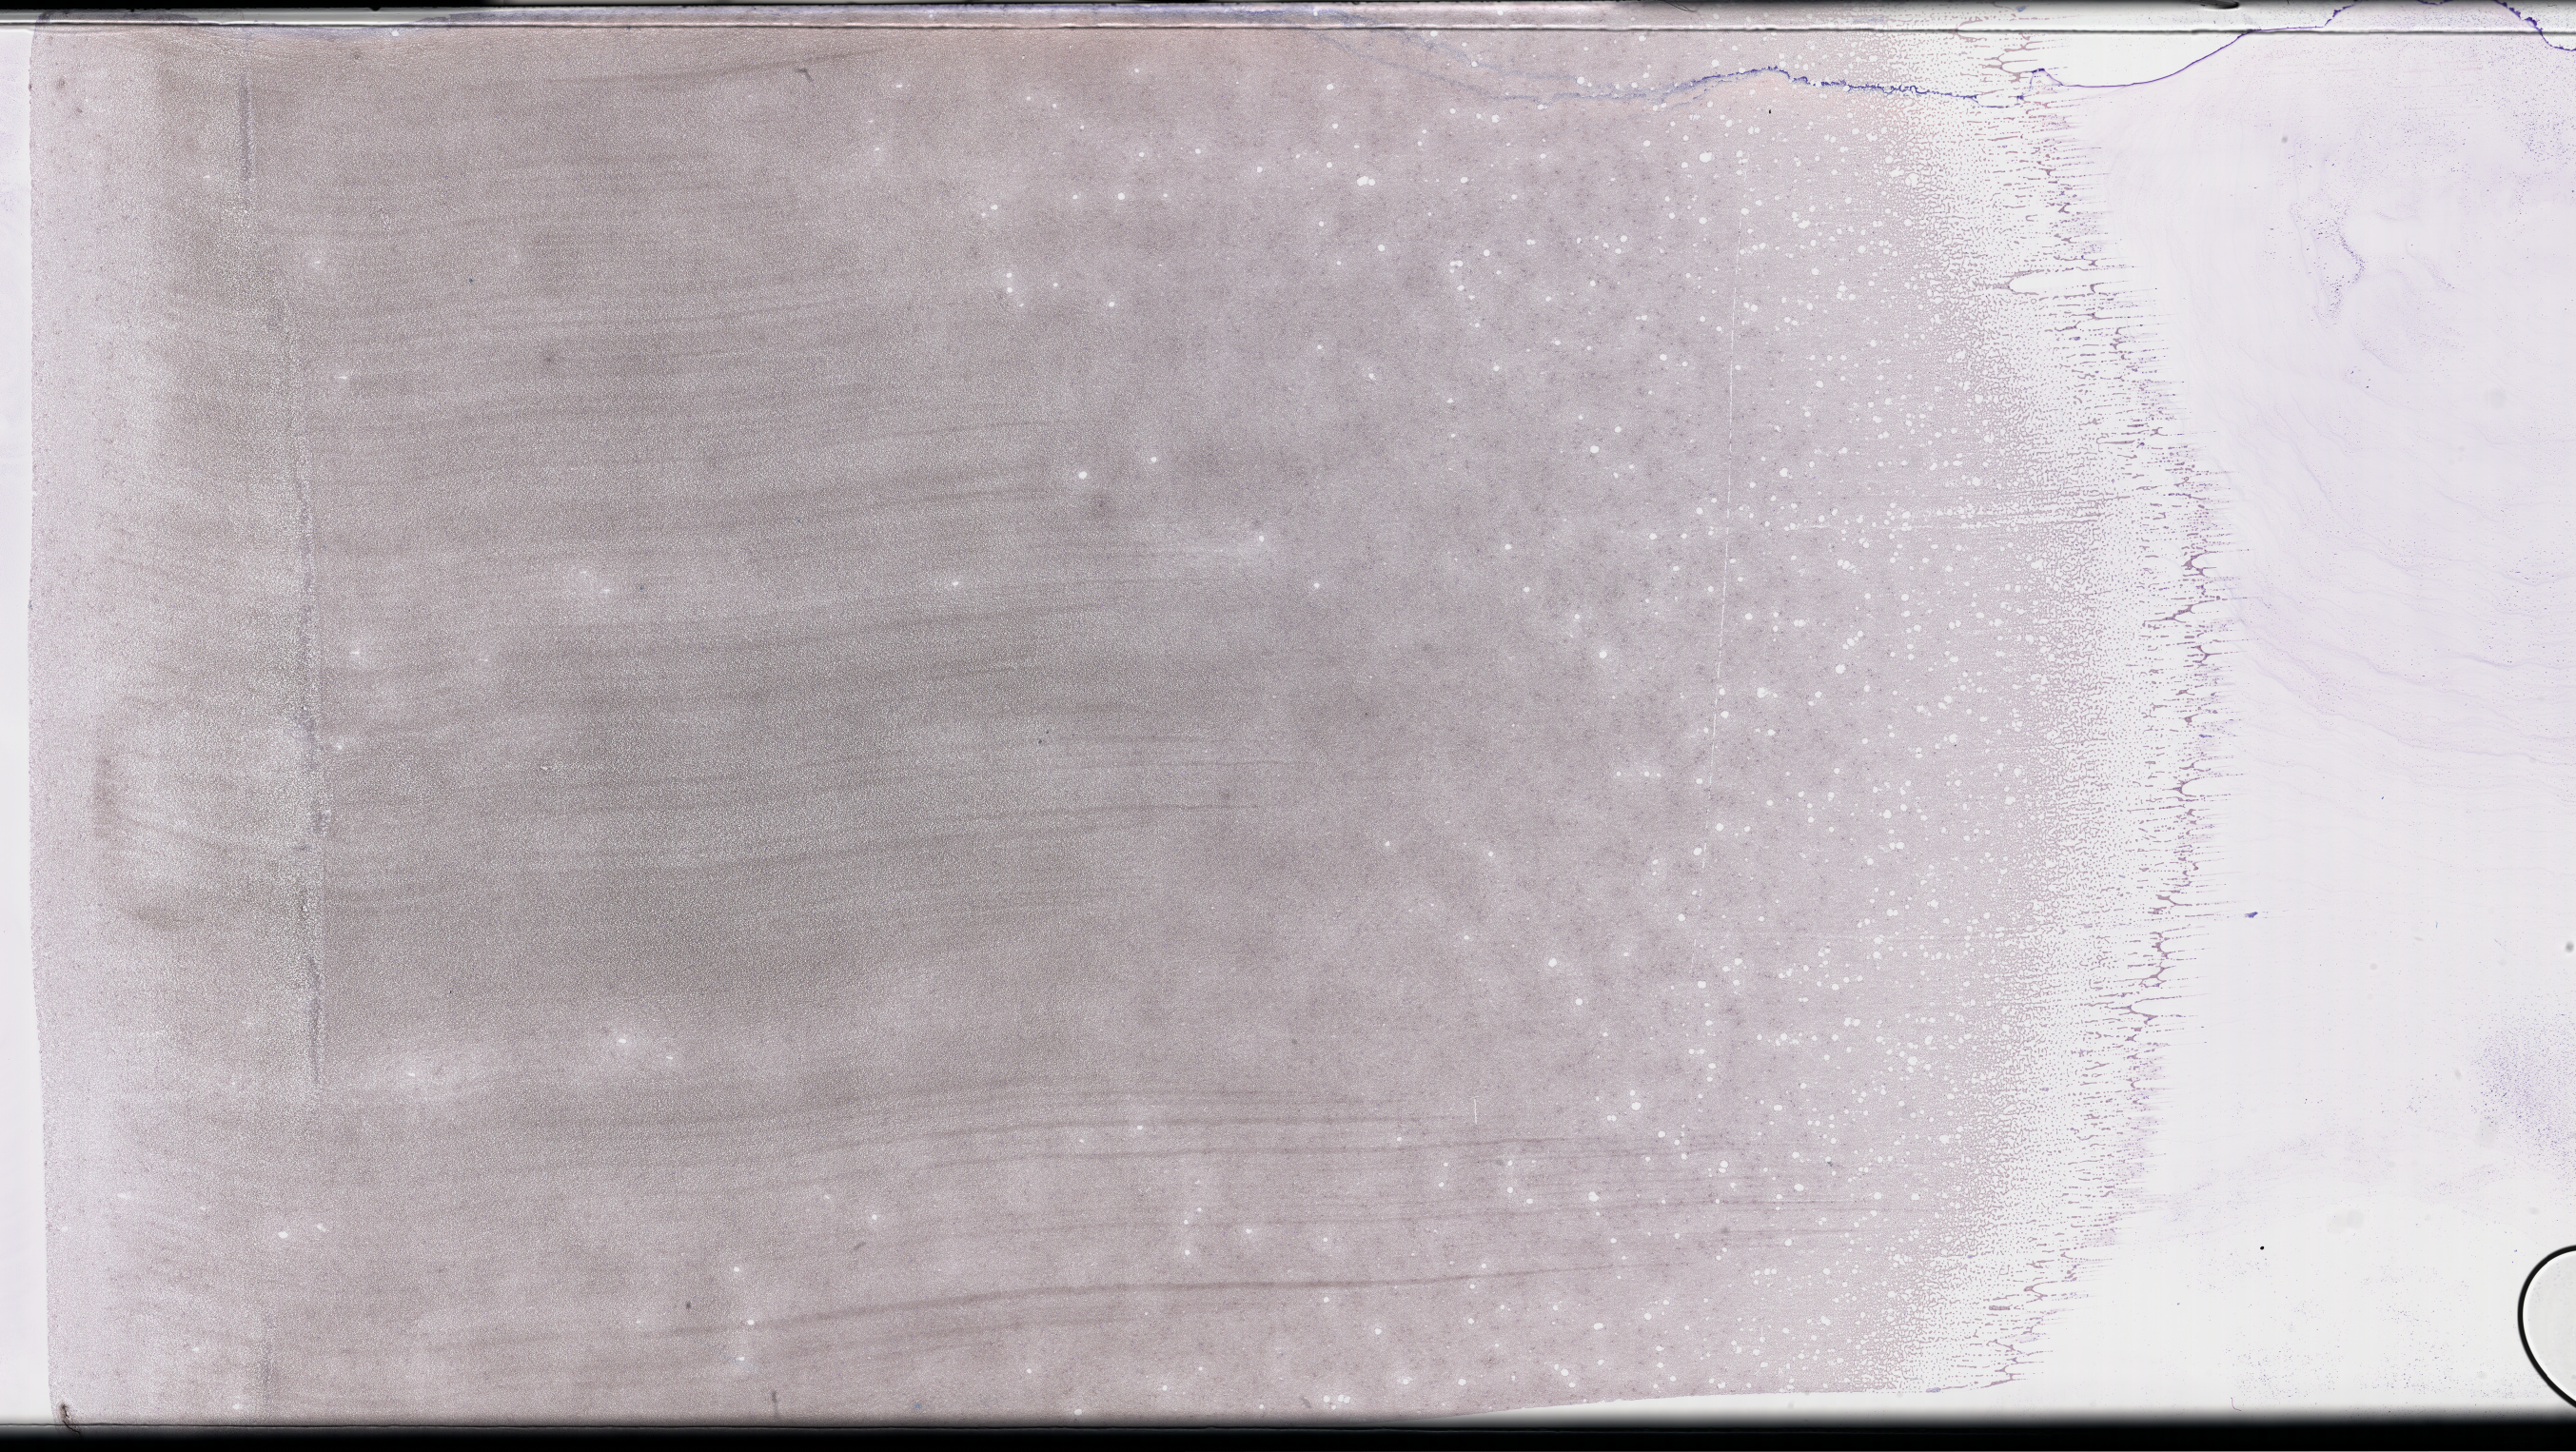
Whole-slide image of a whole blood smear, Wright–Giemsa stain, whole scanned area (about 43.7 x 24.6 mm) shown as a low-resolution overview, EDTA-anticoagulated smear, collected on treatment. Male patient.
From a patient with: Plasma Cell Myeloma.